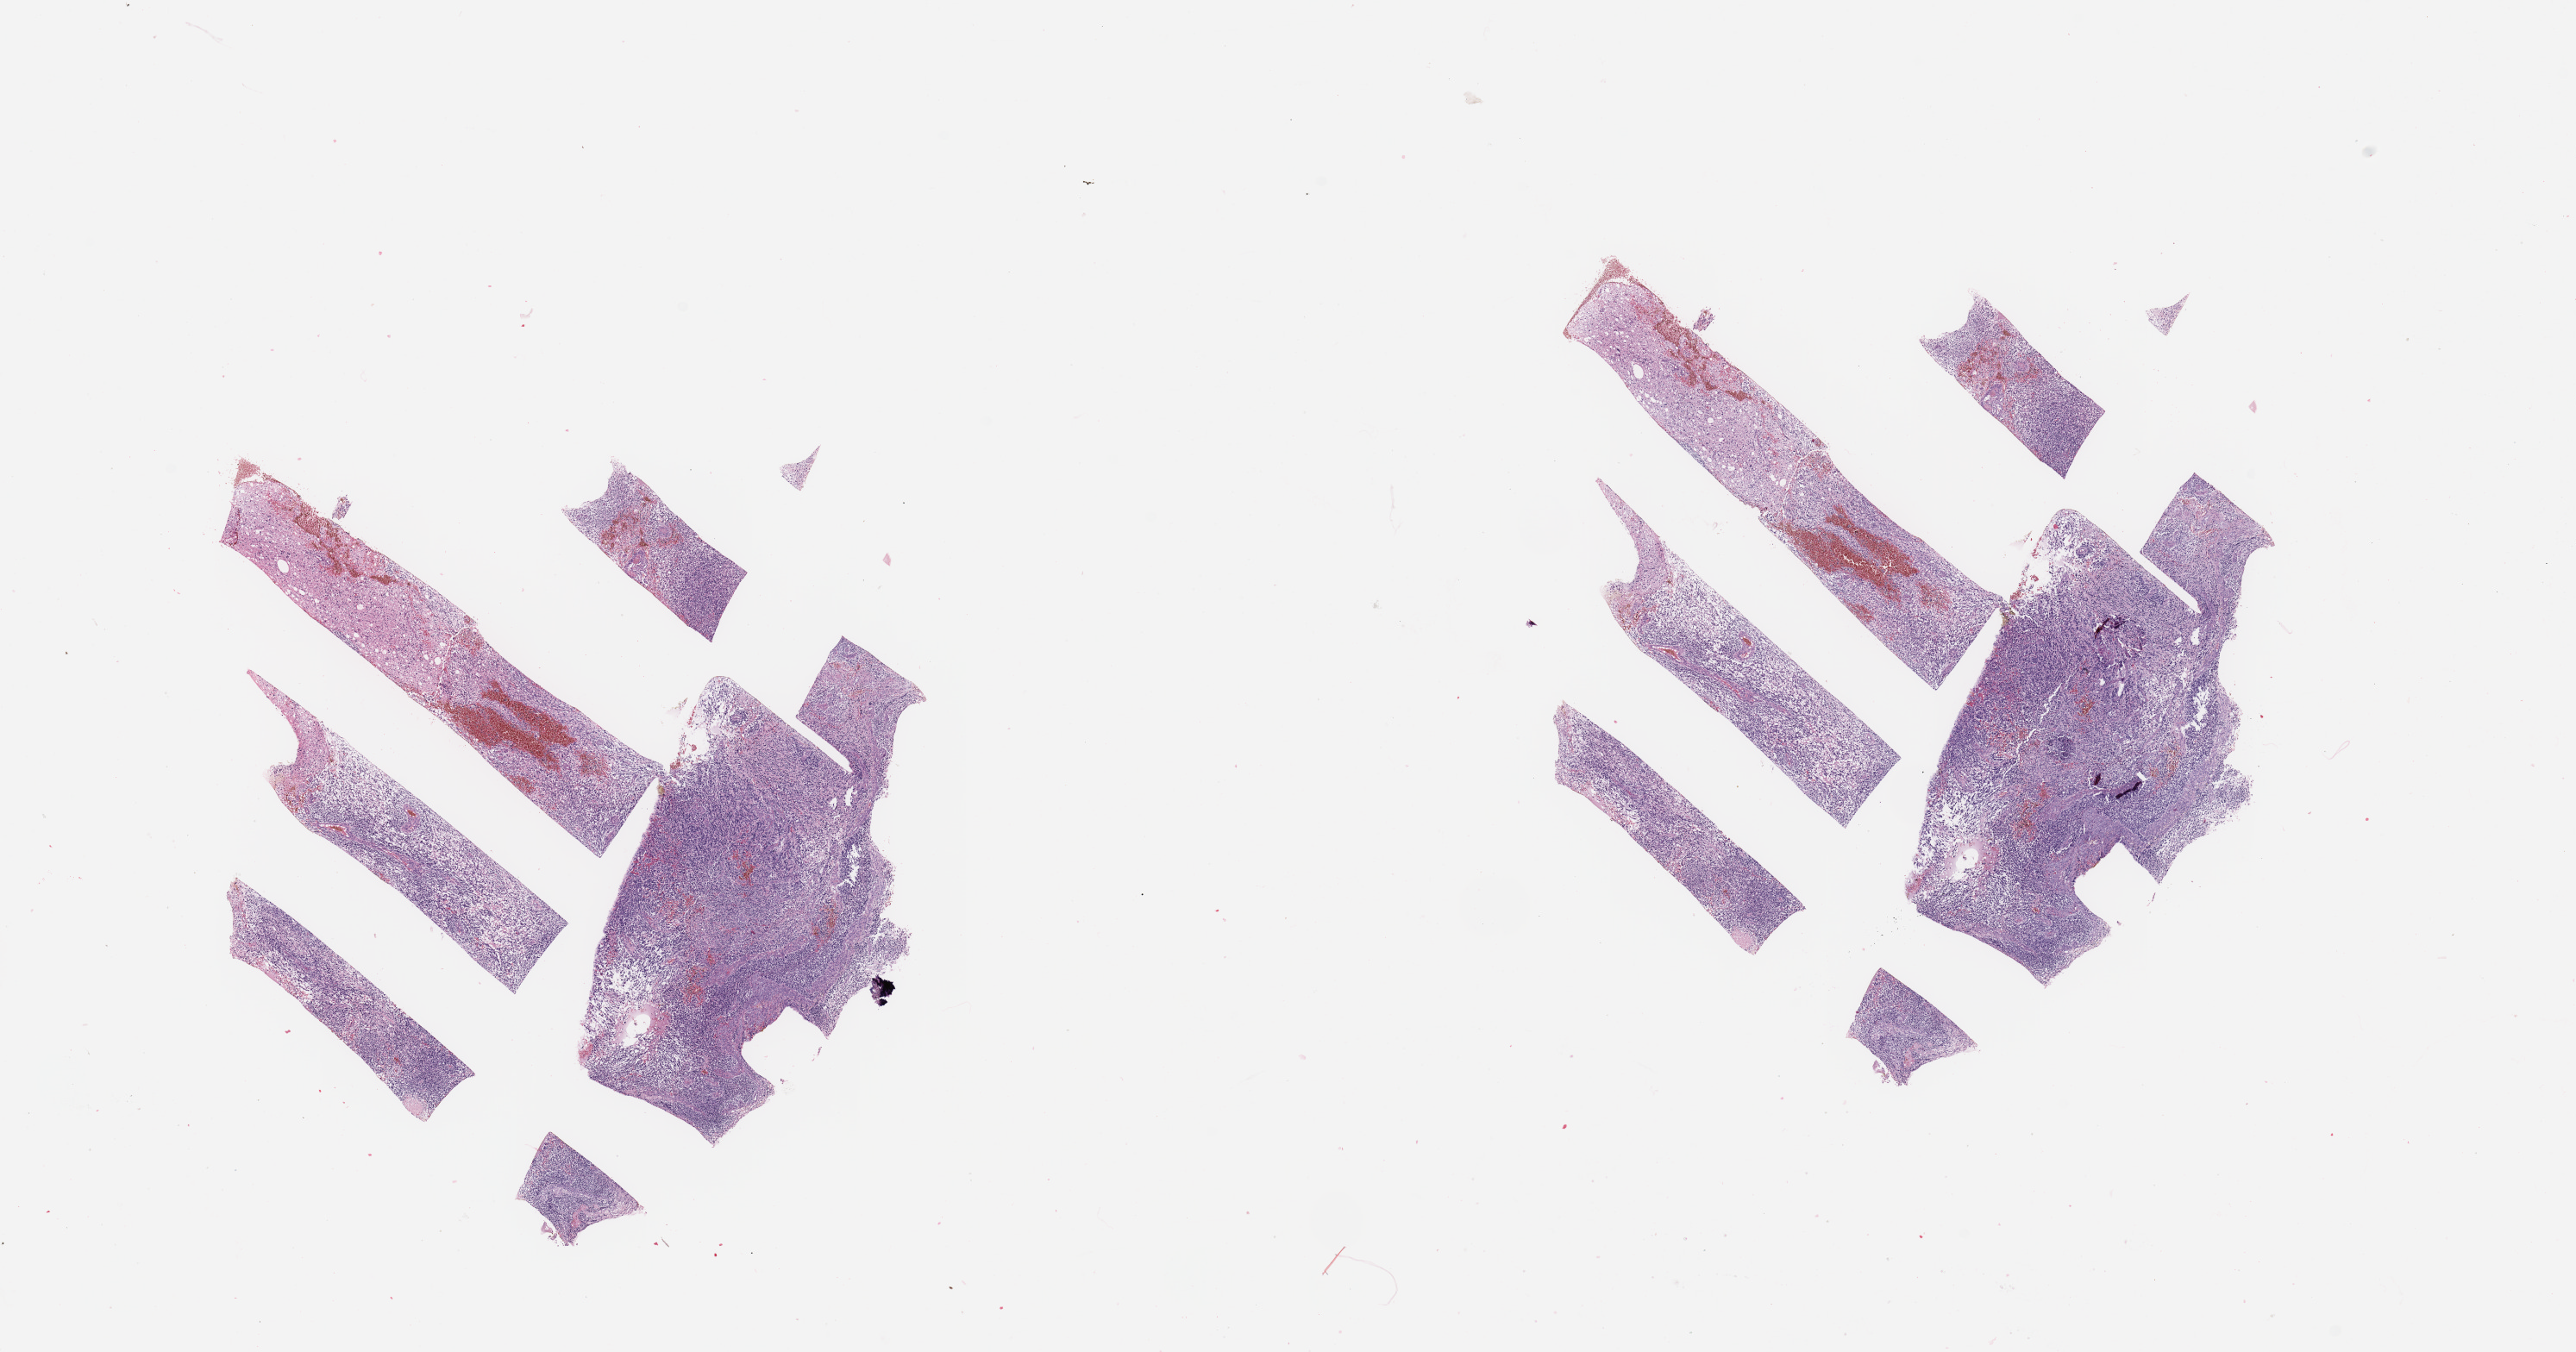
Whole-slide histology image, Hematoxylin and eosin (H&E) stained, whole scanned area (about 23.6 x 12.4 mm) shown as a low-resolution overview, tumour tissue sample, sampled site: brain. Female, 60 y/o. Pathologist review of this section (percent, as recorded): tumour nuclei 75%, necrosis 10%.
Diagnosis: Glioblastoma.